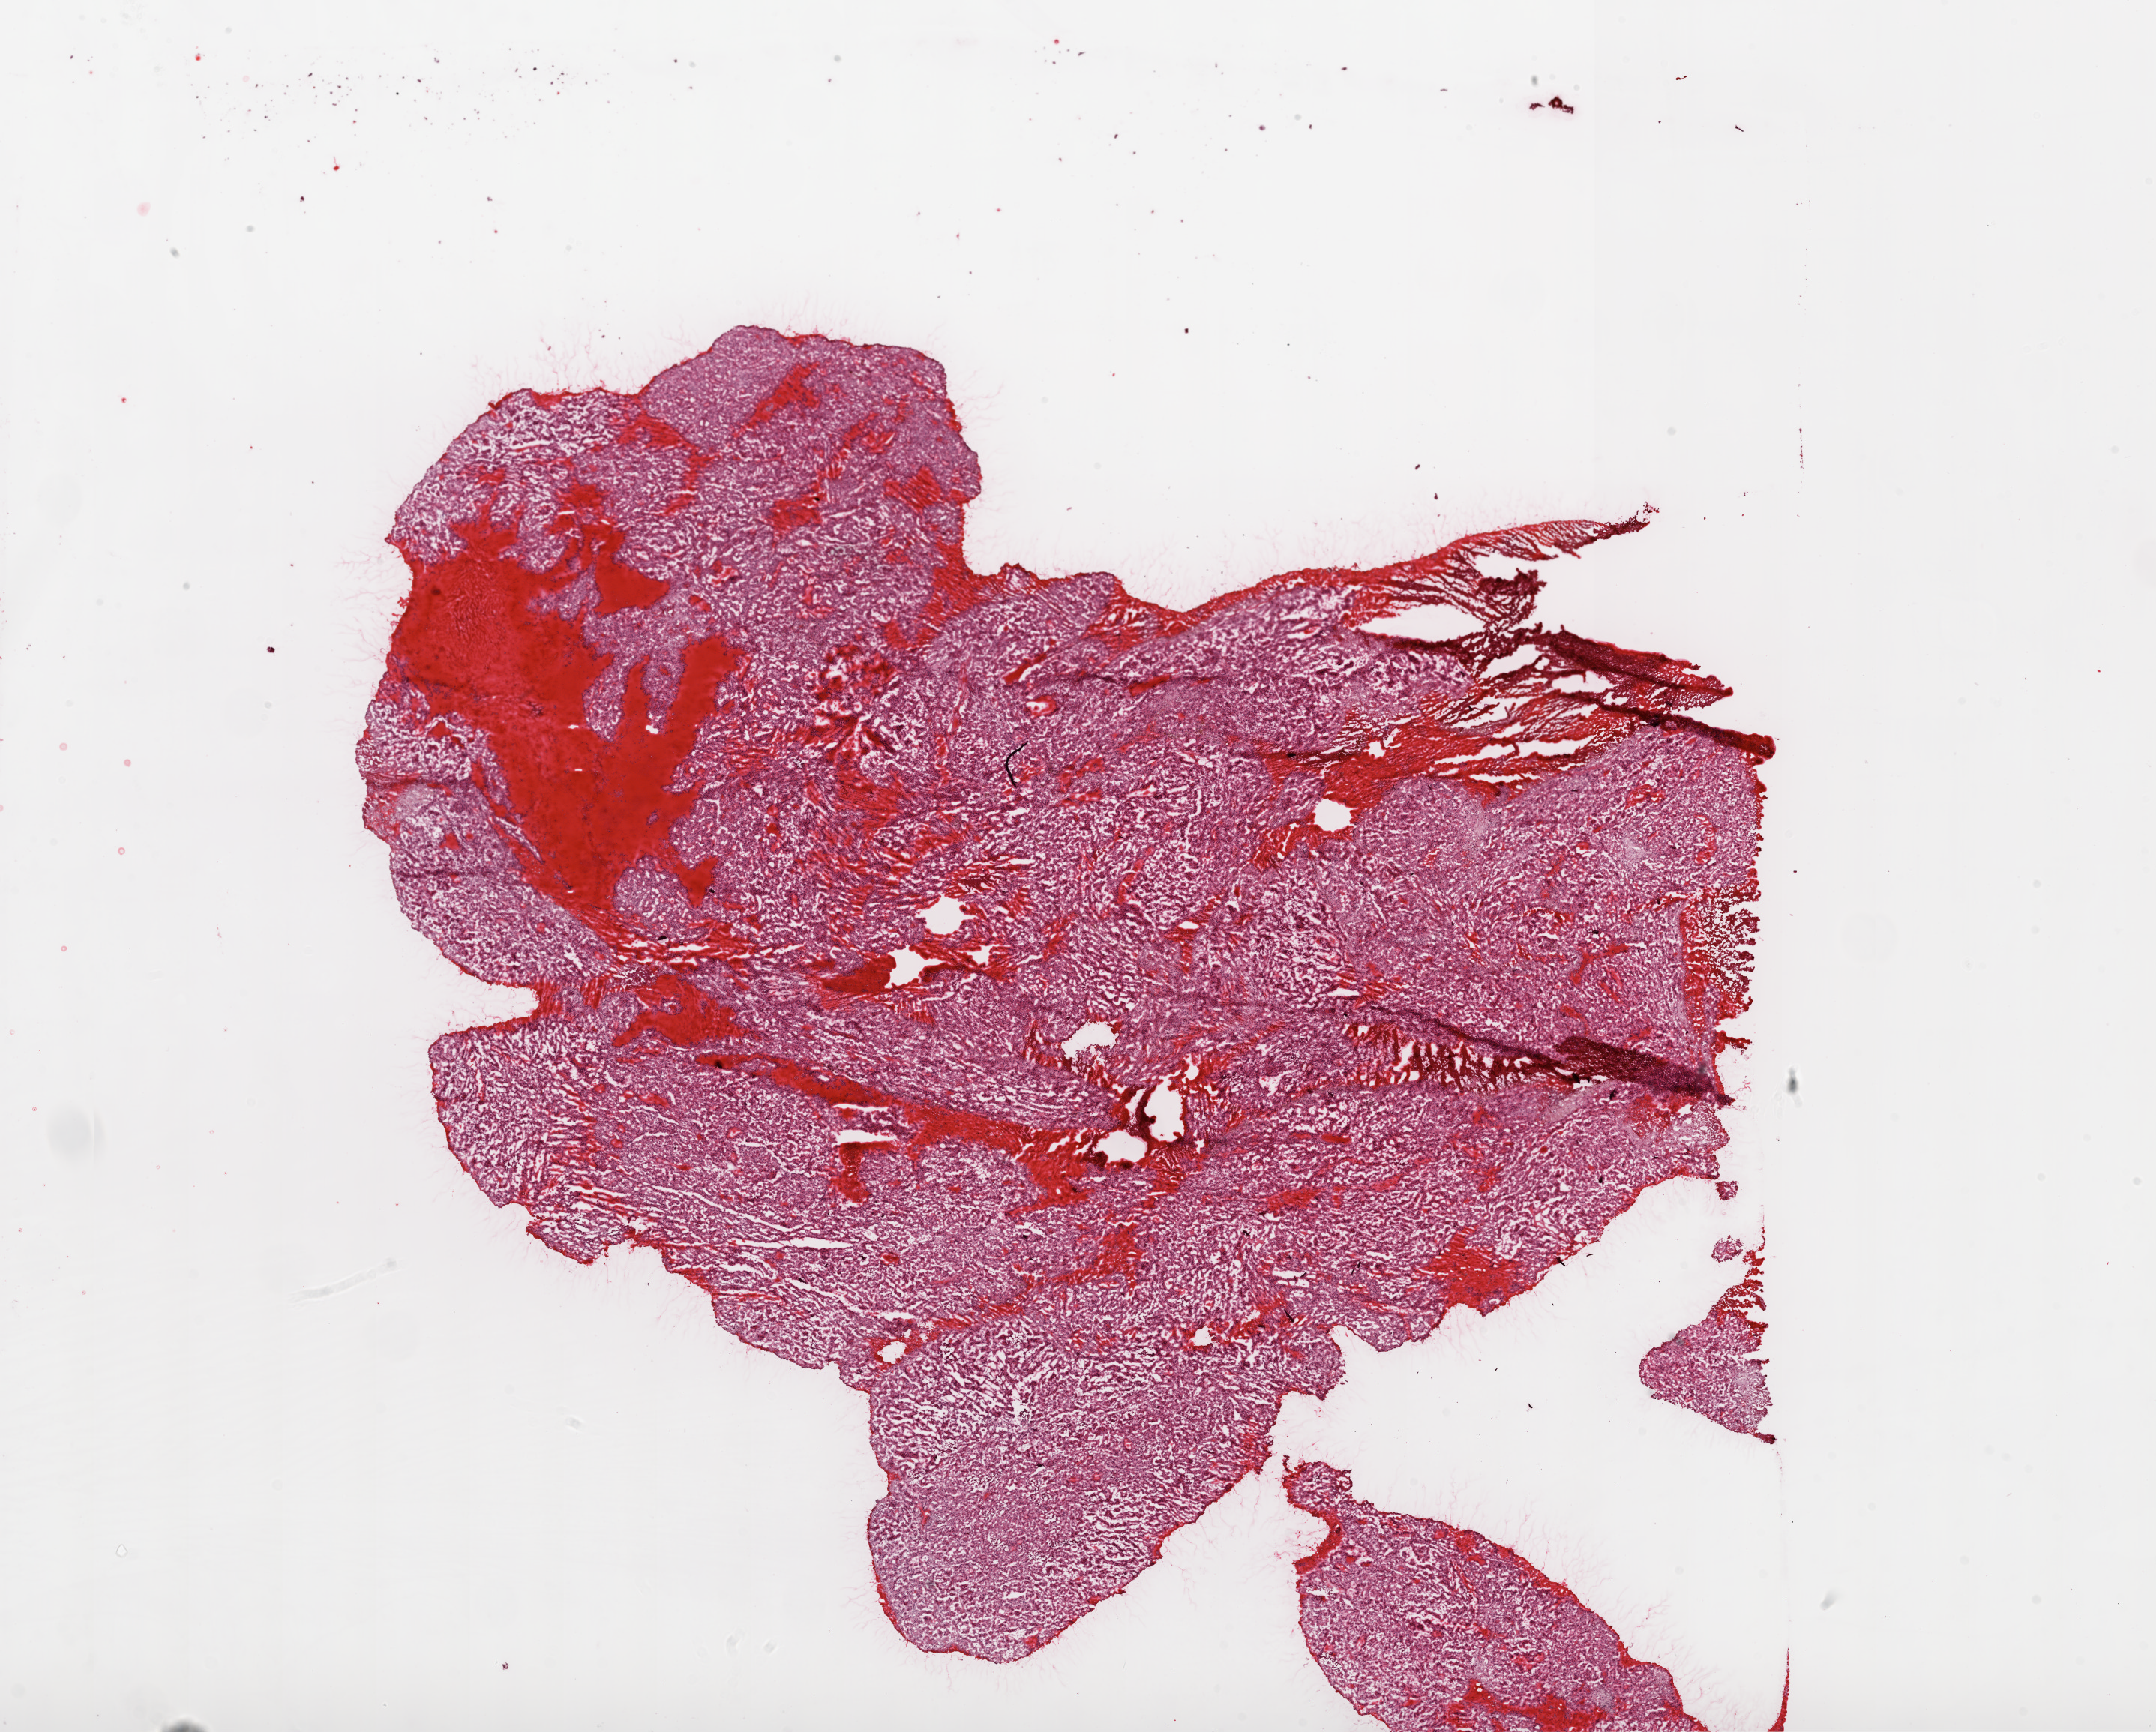
Hematoxylin and eosin (H&E) stained whole-slide image — whole scanned area (about 23.1 x 18.5 mm, from a 20x scan) shown as a low-resolution overview, frozen section, primary tumour sample from the kidney. Female, age 62 years at initial diagnosis. Histologic grade: G2 (moderately differentiated). Slide review estimates, as recorded: tumour cells 100%, tumour nuclei 90%, normal cells 0%, stromal cells 0%, necrosis 0%. Infiltration values recorded for this section: lymphocyte infiltration 2%.
* lymph nodes positive (case pathology): 0 of 1 examined
* AJCC pathologic stage: I
* histologic diagnosis: Clear cell adenocarcinoma, NOS